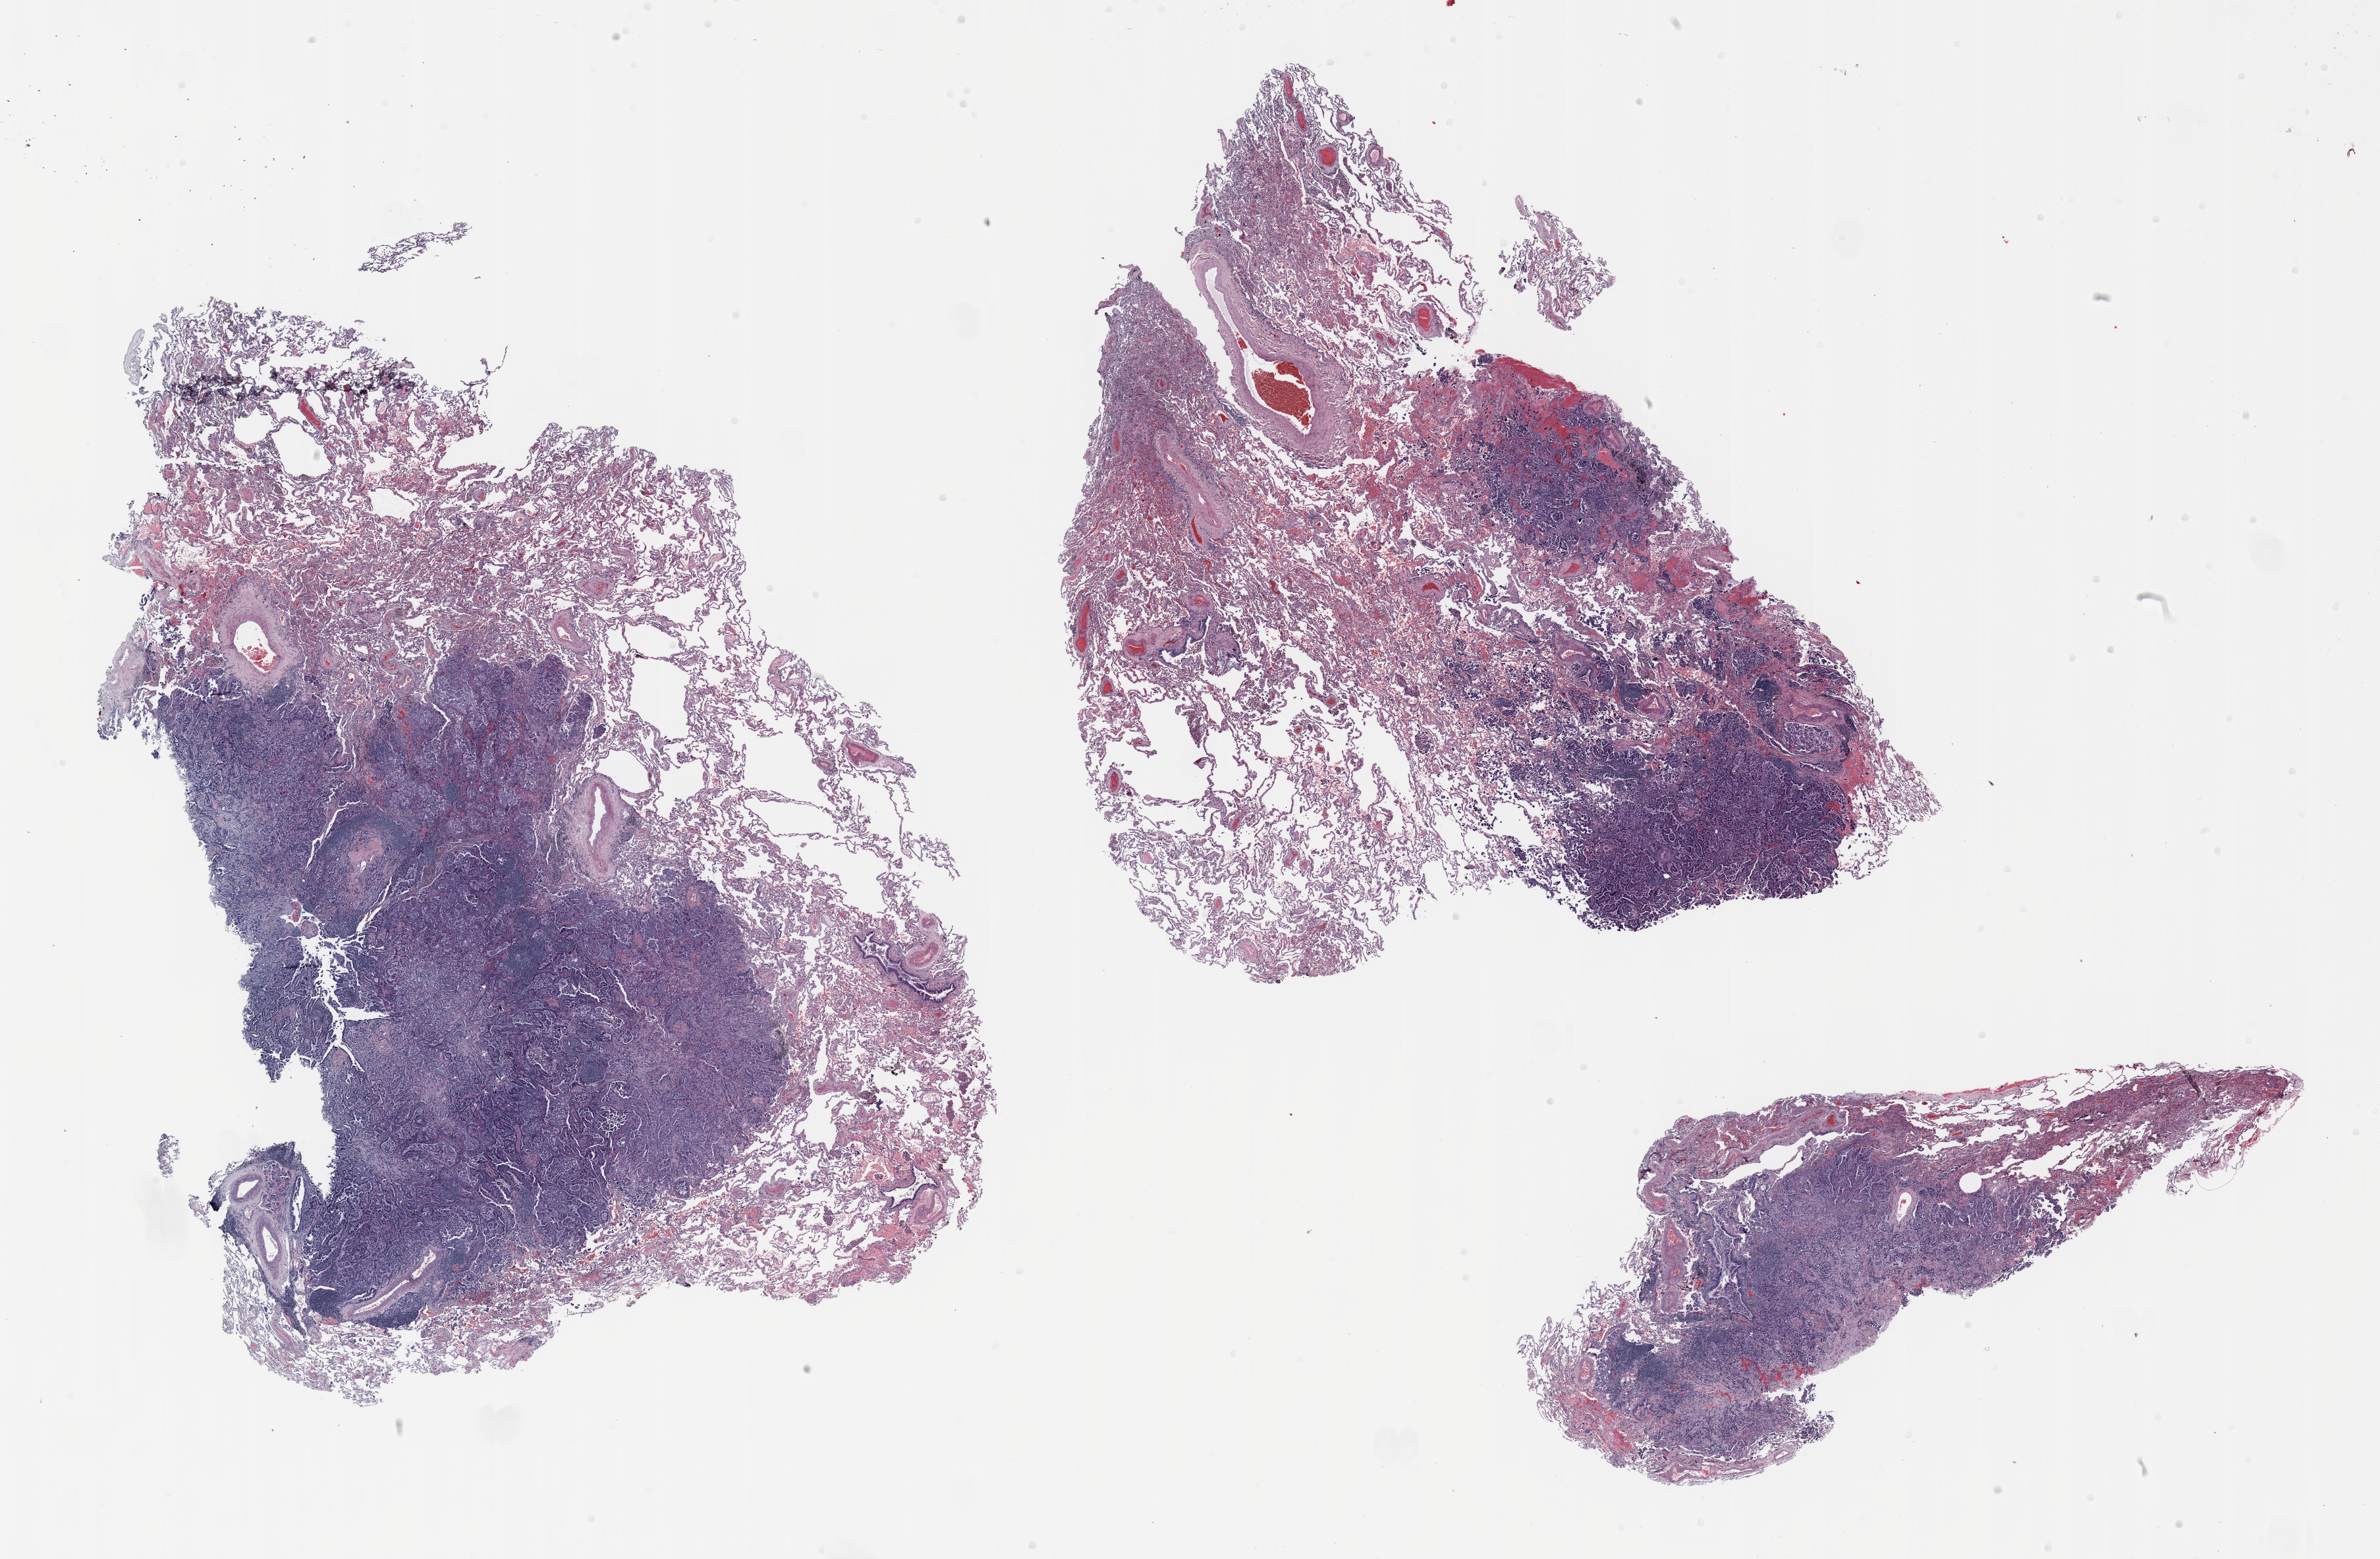
H&E whole-slide image — shown as a low-resolution overview of the whole scanned area (about 29.0 x 19.0 mm, from a 20x scan); formalin-fixed paraffin-embedded (FFPE) section; lung tissue. Male, age 65 at enrolment. Grade: moderately differentiated (G2).
Participant's lung-cancer diagnosis: Adenocarcinoma, NOS (ICD-O-3 8140/3). Tumour size (pathology): 15 mm. Stage (AJCC 6th edition): IA. Primary tumour location (clinical record): right middle lobe.